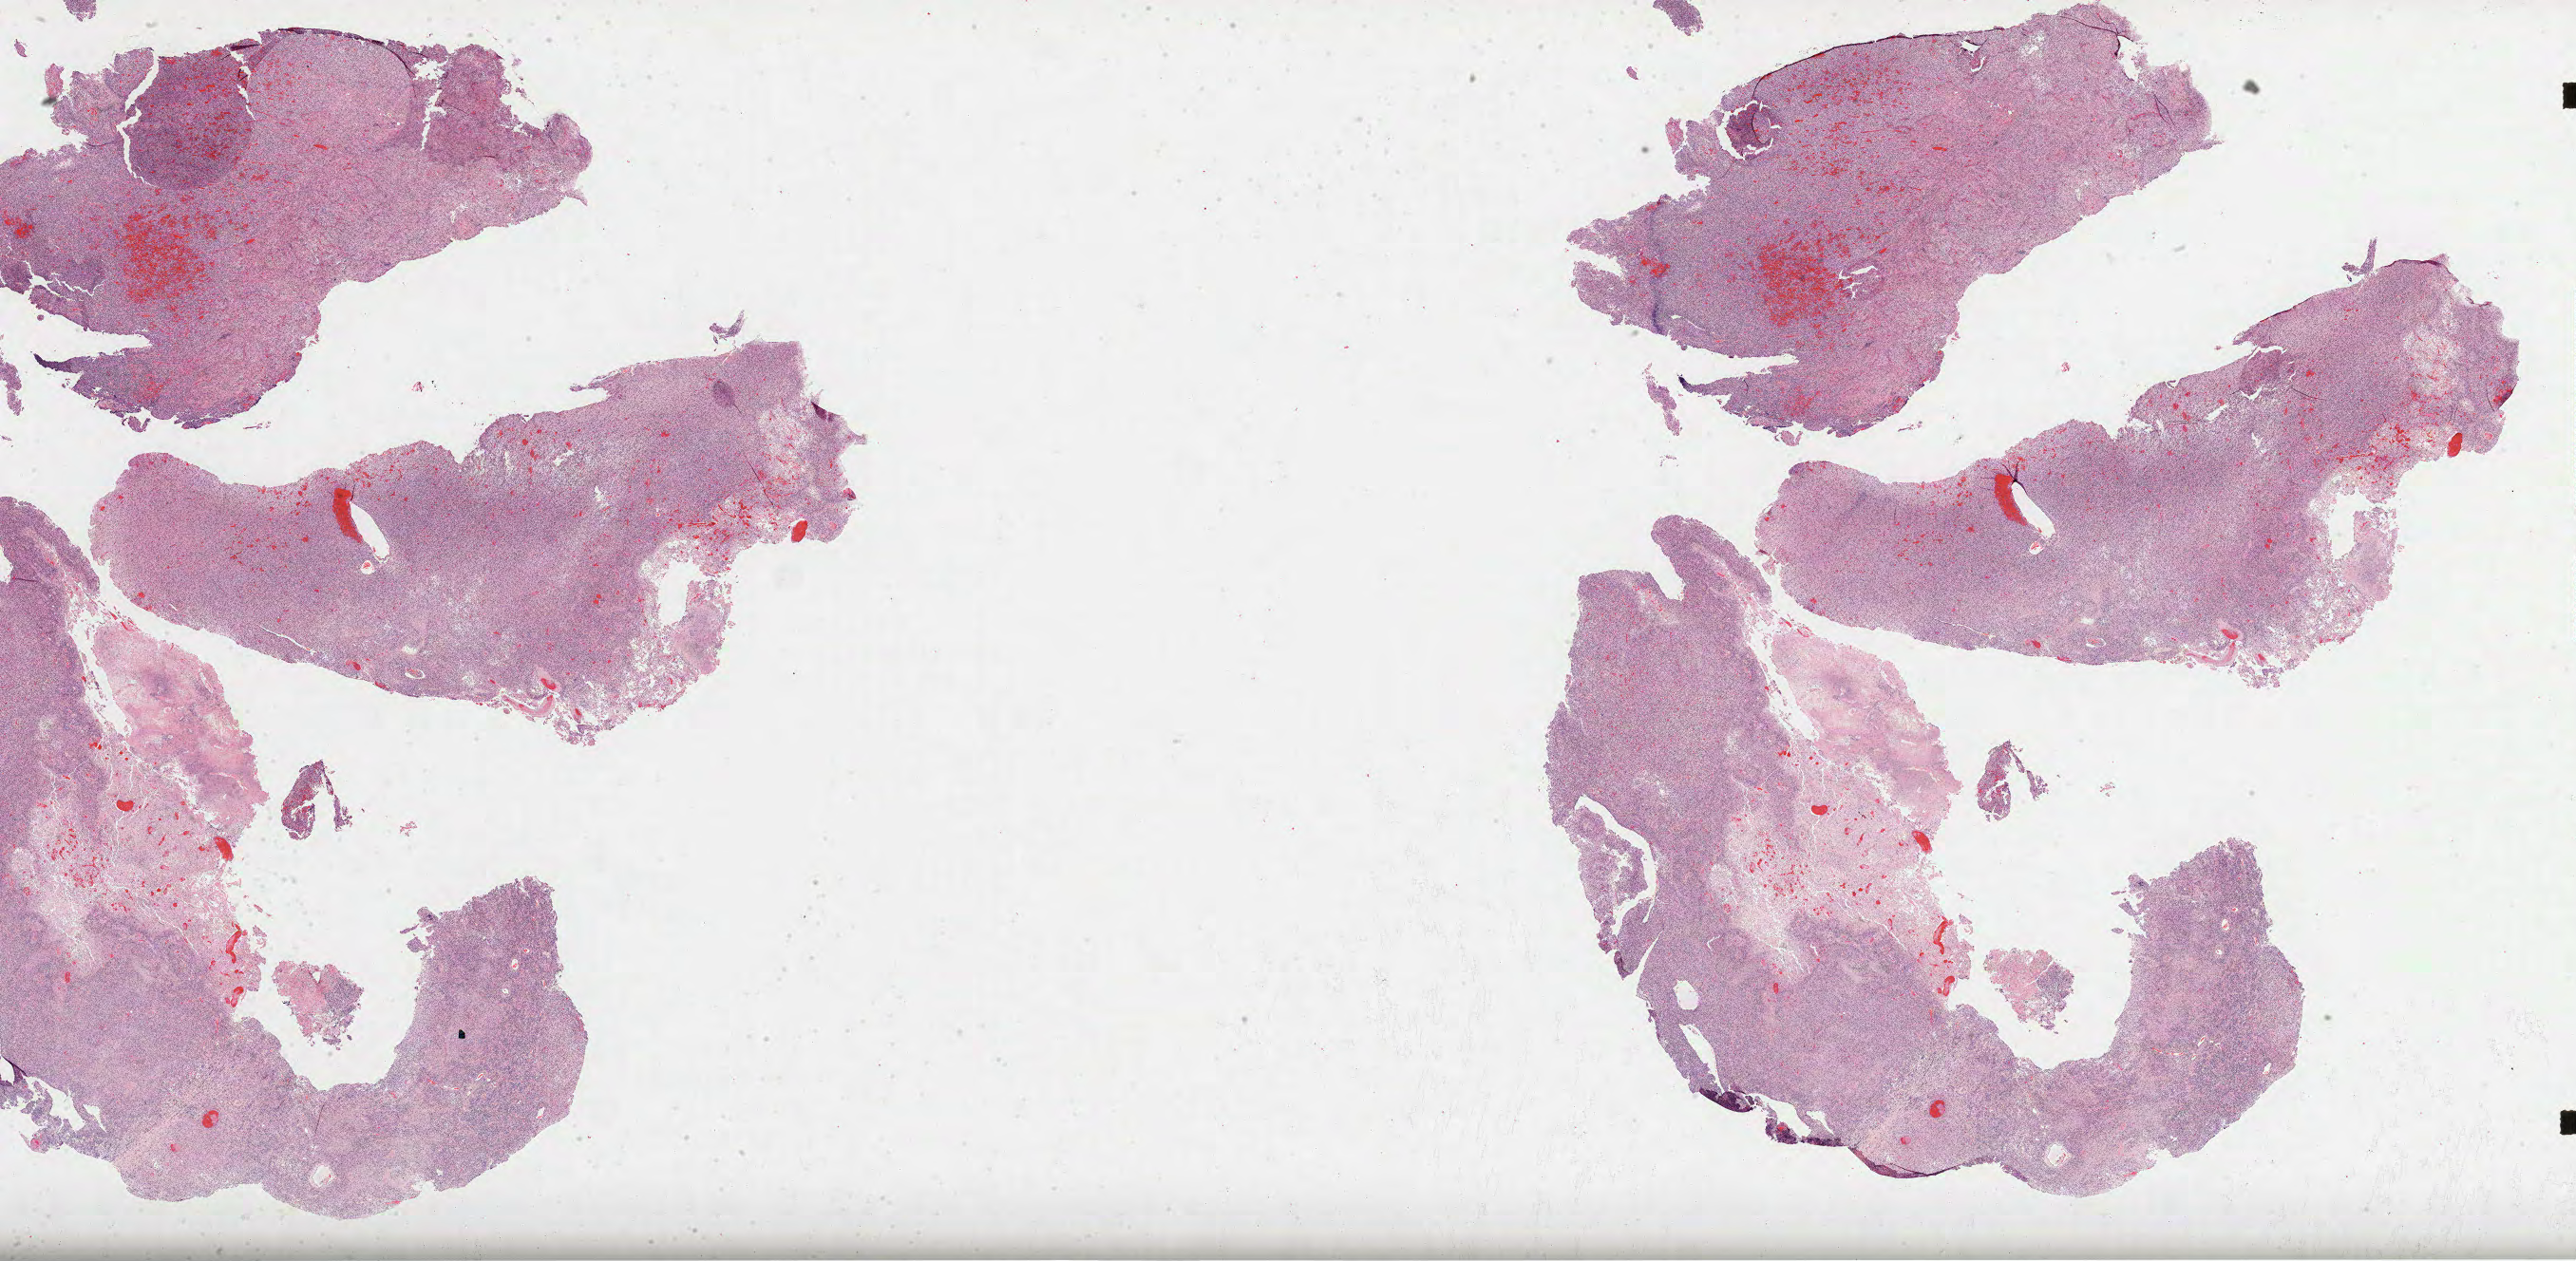
Hematoxylin and eosin (H&E) stained whole-slide image — whole scanned area (about 43.8 x 21.4 mm, slide scanned at 40x) shown as a low-resolution overview; formalin-fixed paraffin-embedded (FFPE) diagnostic section; sample: primary tumour, brain. Patient: female, age at initial diagnosis 72 years.
Pathologic diagnosis: Glioblastoma.